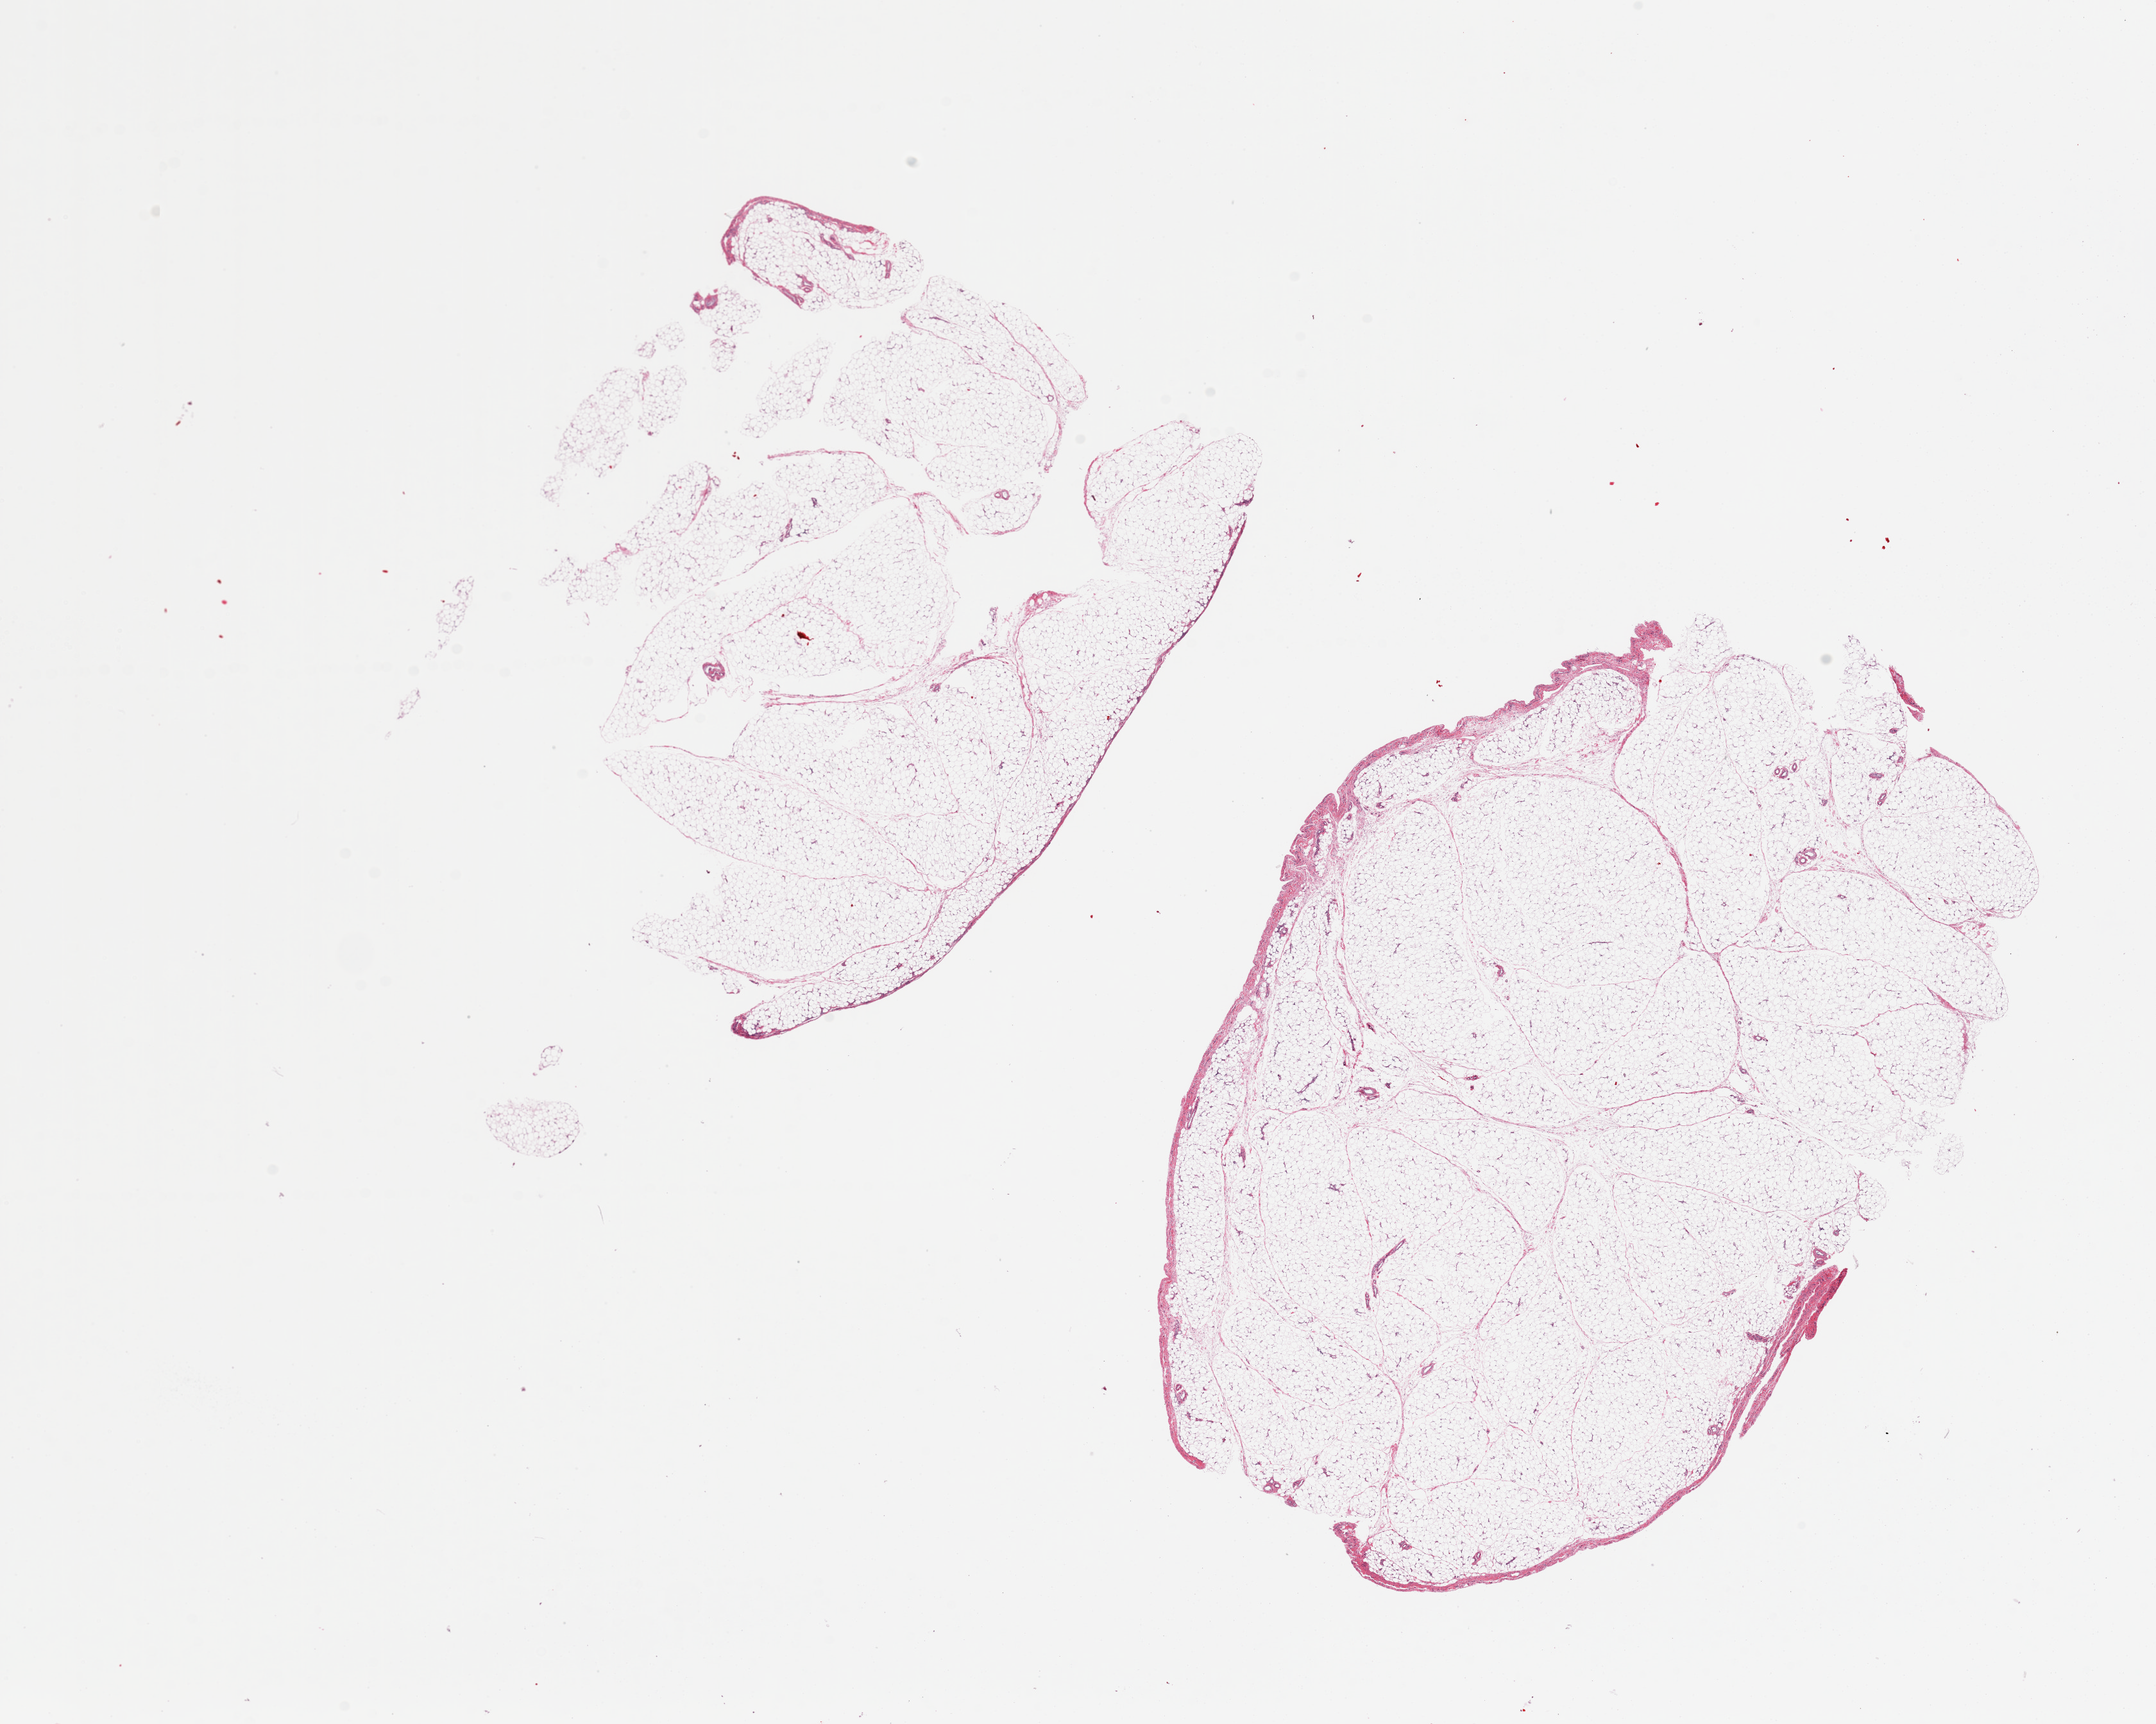
Whole-slide image, H&E stain, a low-resolution overview of the entire scanned area, about 26.6 x 21.2 mm, PAXgene-fixed, paraffin-embedded tissue, sampled site (target tissue): omentum, tissue donor sample.
Review note (as recorded): 2 pieces.